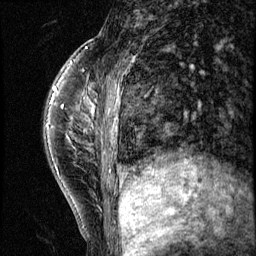
Breast MRI (dynamic contrast-enhanced), one sagittal slice; 3 images stored at this slice position (order not interpretable as contrast timing); 1.5 T; TE 4.2 ms, TR 8.7 ms; 2.5 mm slice thickness; 256 × 256 image matrix, field of view 180 × 180 mm. Female patient, age 35 years. Case-level facts recorded for this patient, not image findings: setting: breast cancer imaged before/during neoadjuvant chemotherapy; receptor status: HER2-positive.
Structures marked on this image (semi-automatically segmented with operator editing):
- analysis volume of interest (the breast-tissue region the enhancement analysis was run in; not a lesion): box from (x=58, y=84) to (x=138, y=186) px
- tumour enhancement mask (voxels above the 140 % enhancement threshold inside the analysis volume of interest): (x=62, y=85)–(x=117, y=171)